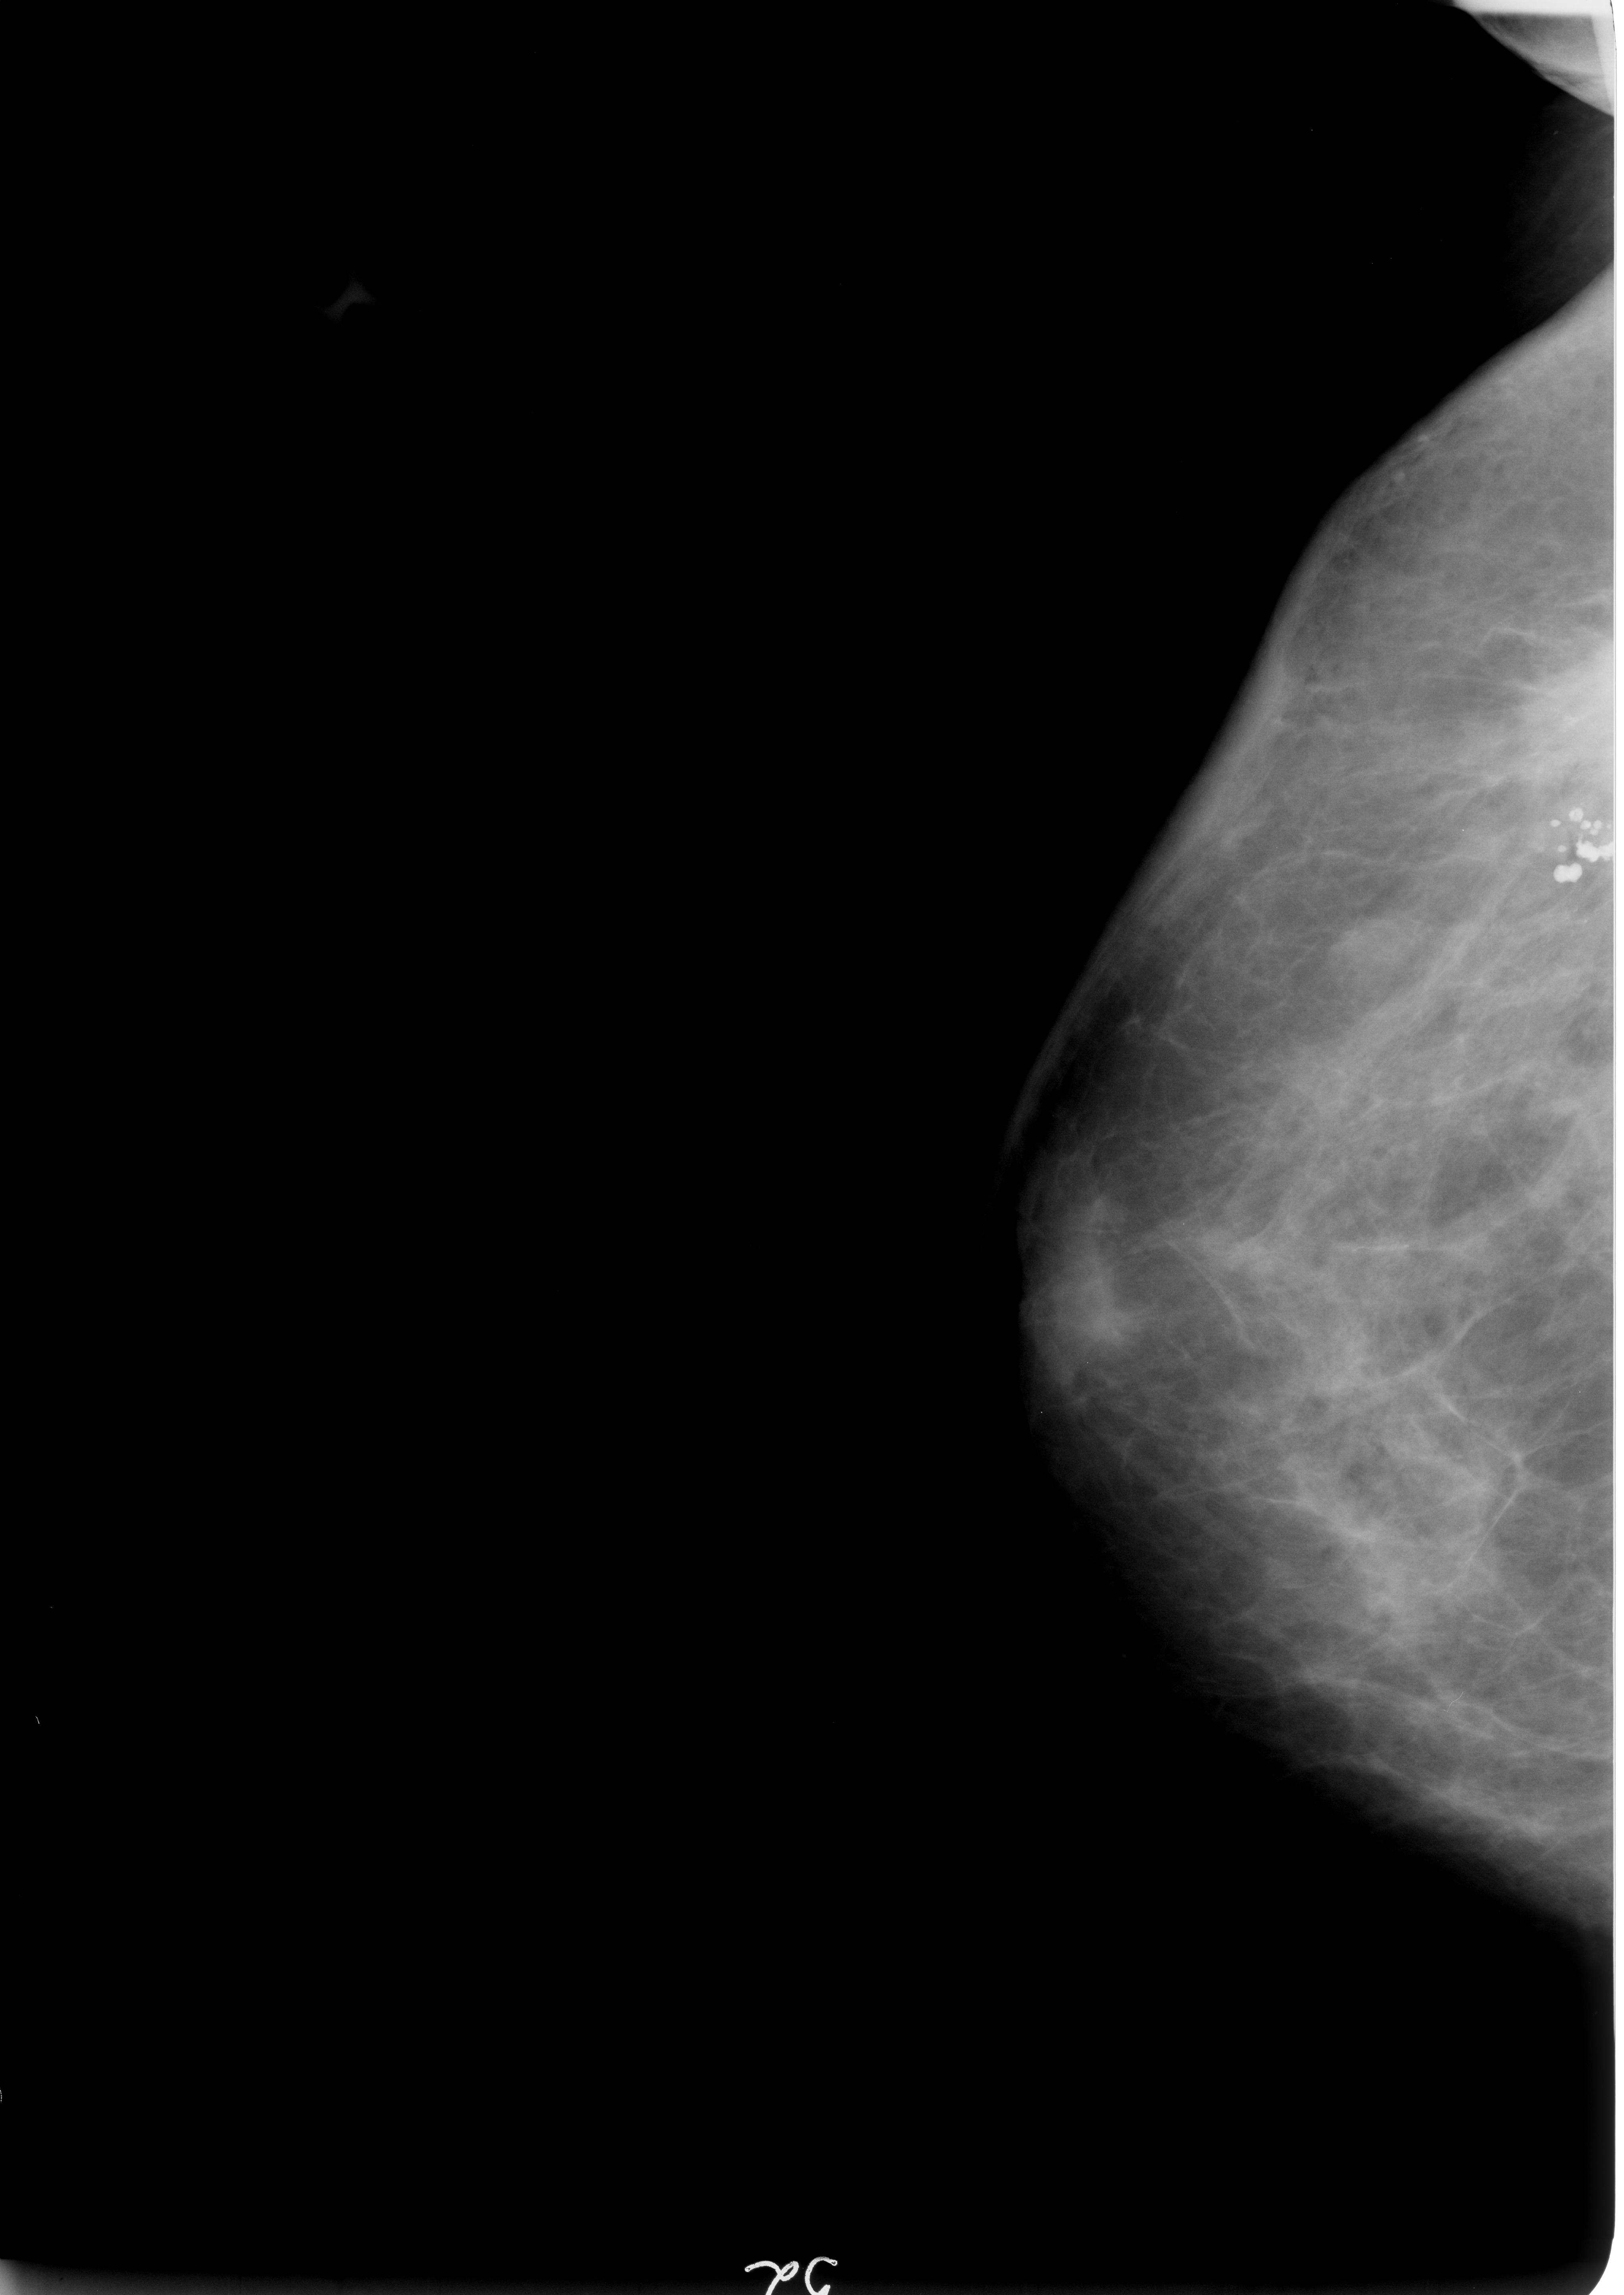
Digitized screen-film mammogram, right breast, craniocaudal (CC) view, BI-RADS breast density category 2 (scale 1–4).
Abnormality record for this image: Finding 1 of 2: calcifications, morphology pleomorphic / fine linear branching, distribution segmental; BI-RADS assessment category 5; pathology (as recorded): malignant. Finding 2 of 2: calcifications, morphology pleomorphic / fine linear branching, distribution segmental; BI-RADS assessment category 5; subtlety rating 5 on a 1 (subtle) to 5 (obvious) scale; pathology (as recorded): malignant.